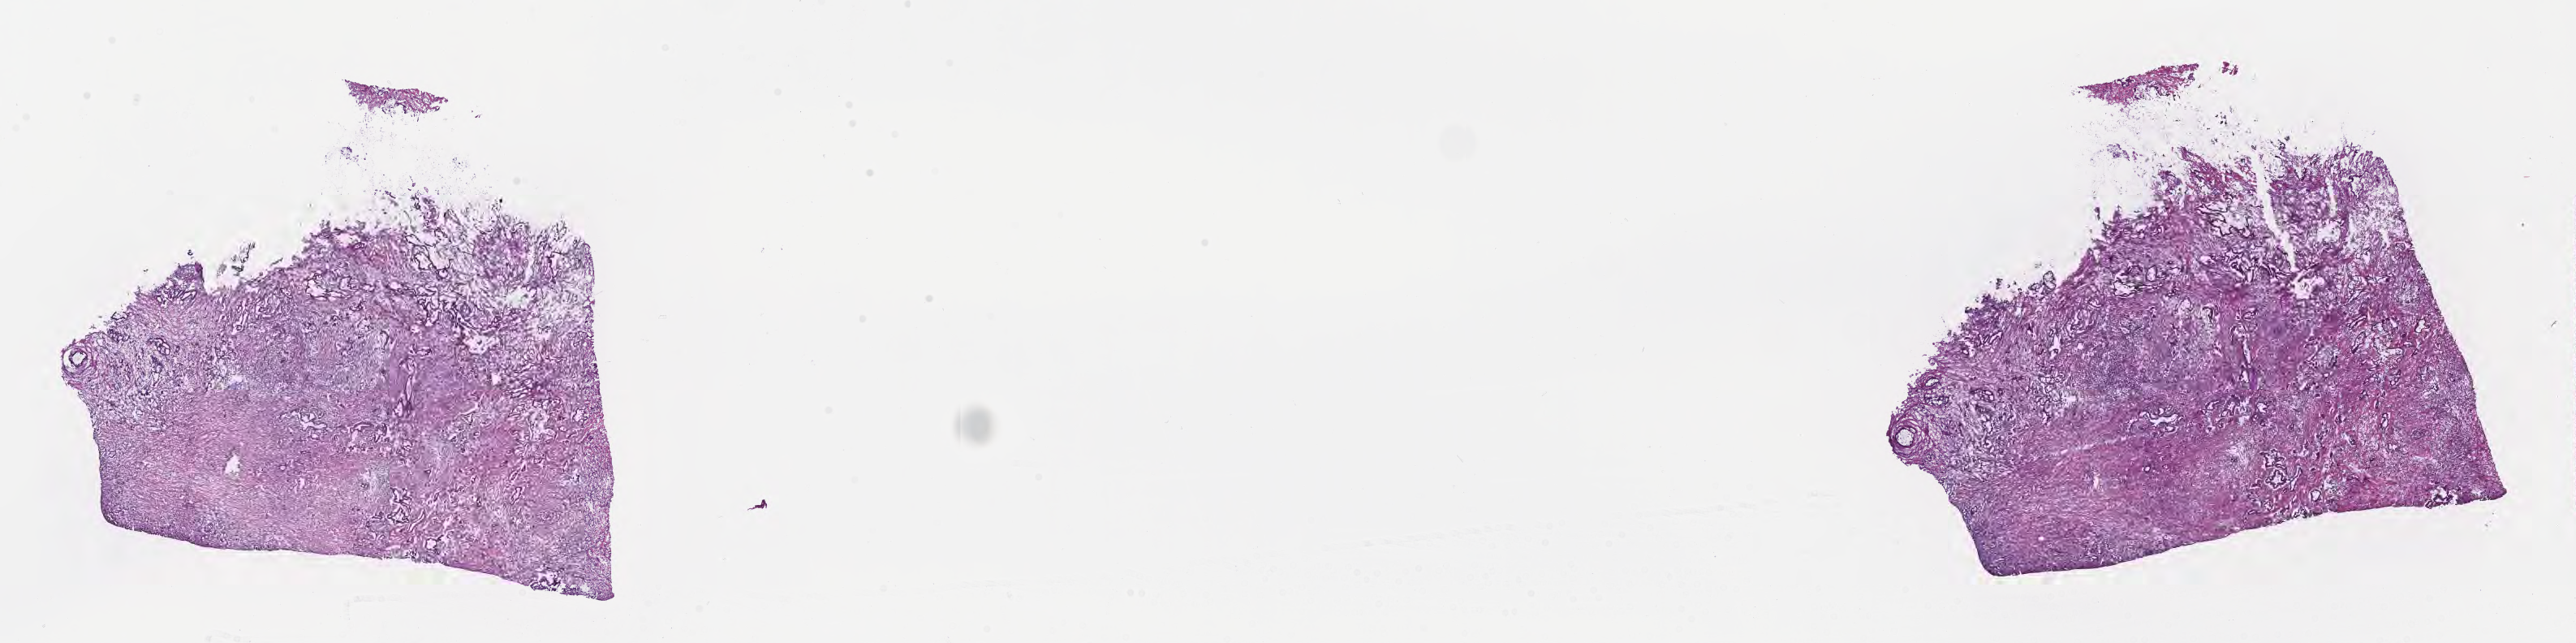
Digitized hematoxylin and eosin (H&E)-stained section, a low-resolution overview of the entire scanned area, about 25.7 x 6.4 mm; frozen section; specimen: primary tumor; anatomic site: tail of pancreas. Male, age 72 years at initial diagnosis.
Histologic diagnosis: Infiltrating duct carcinoma, NOS.